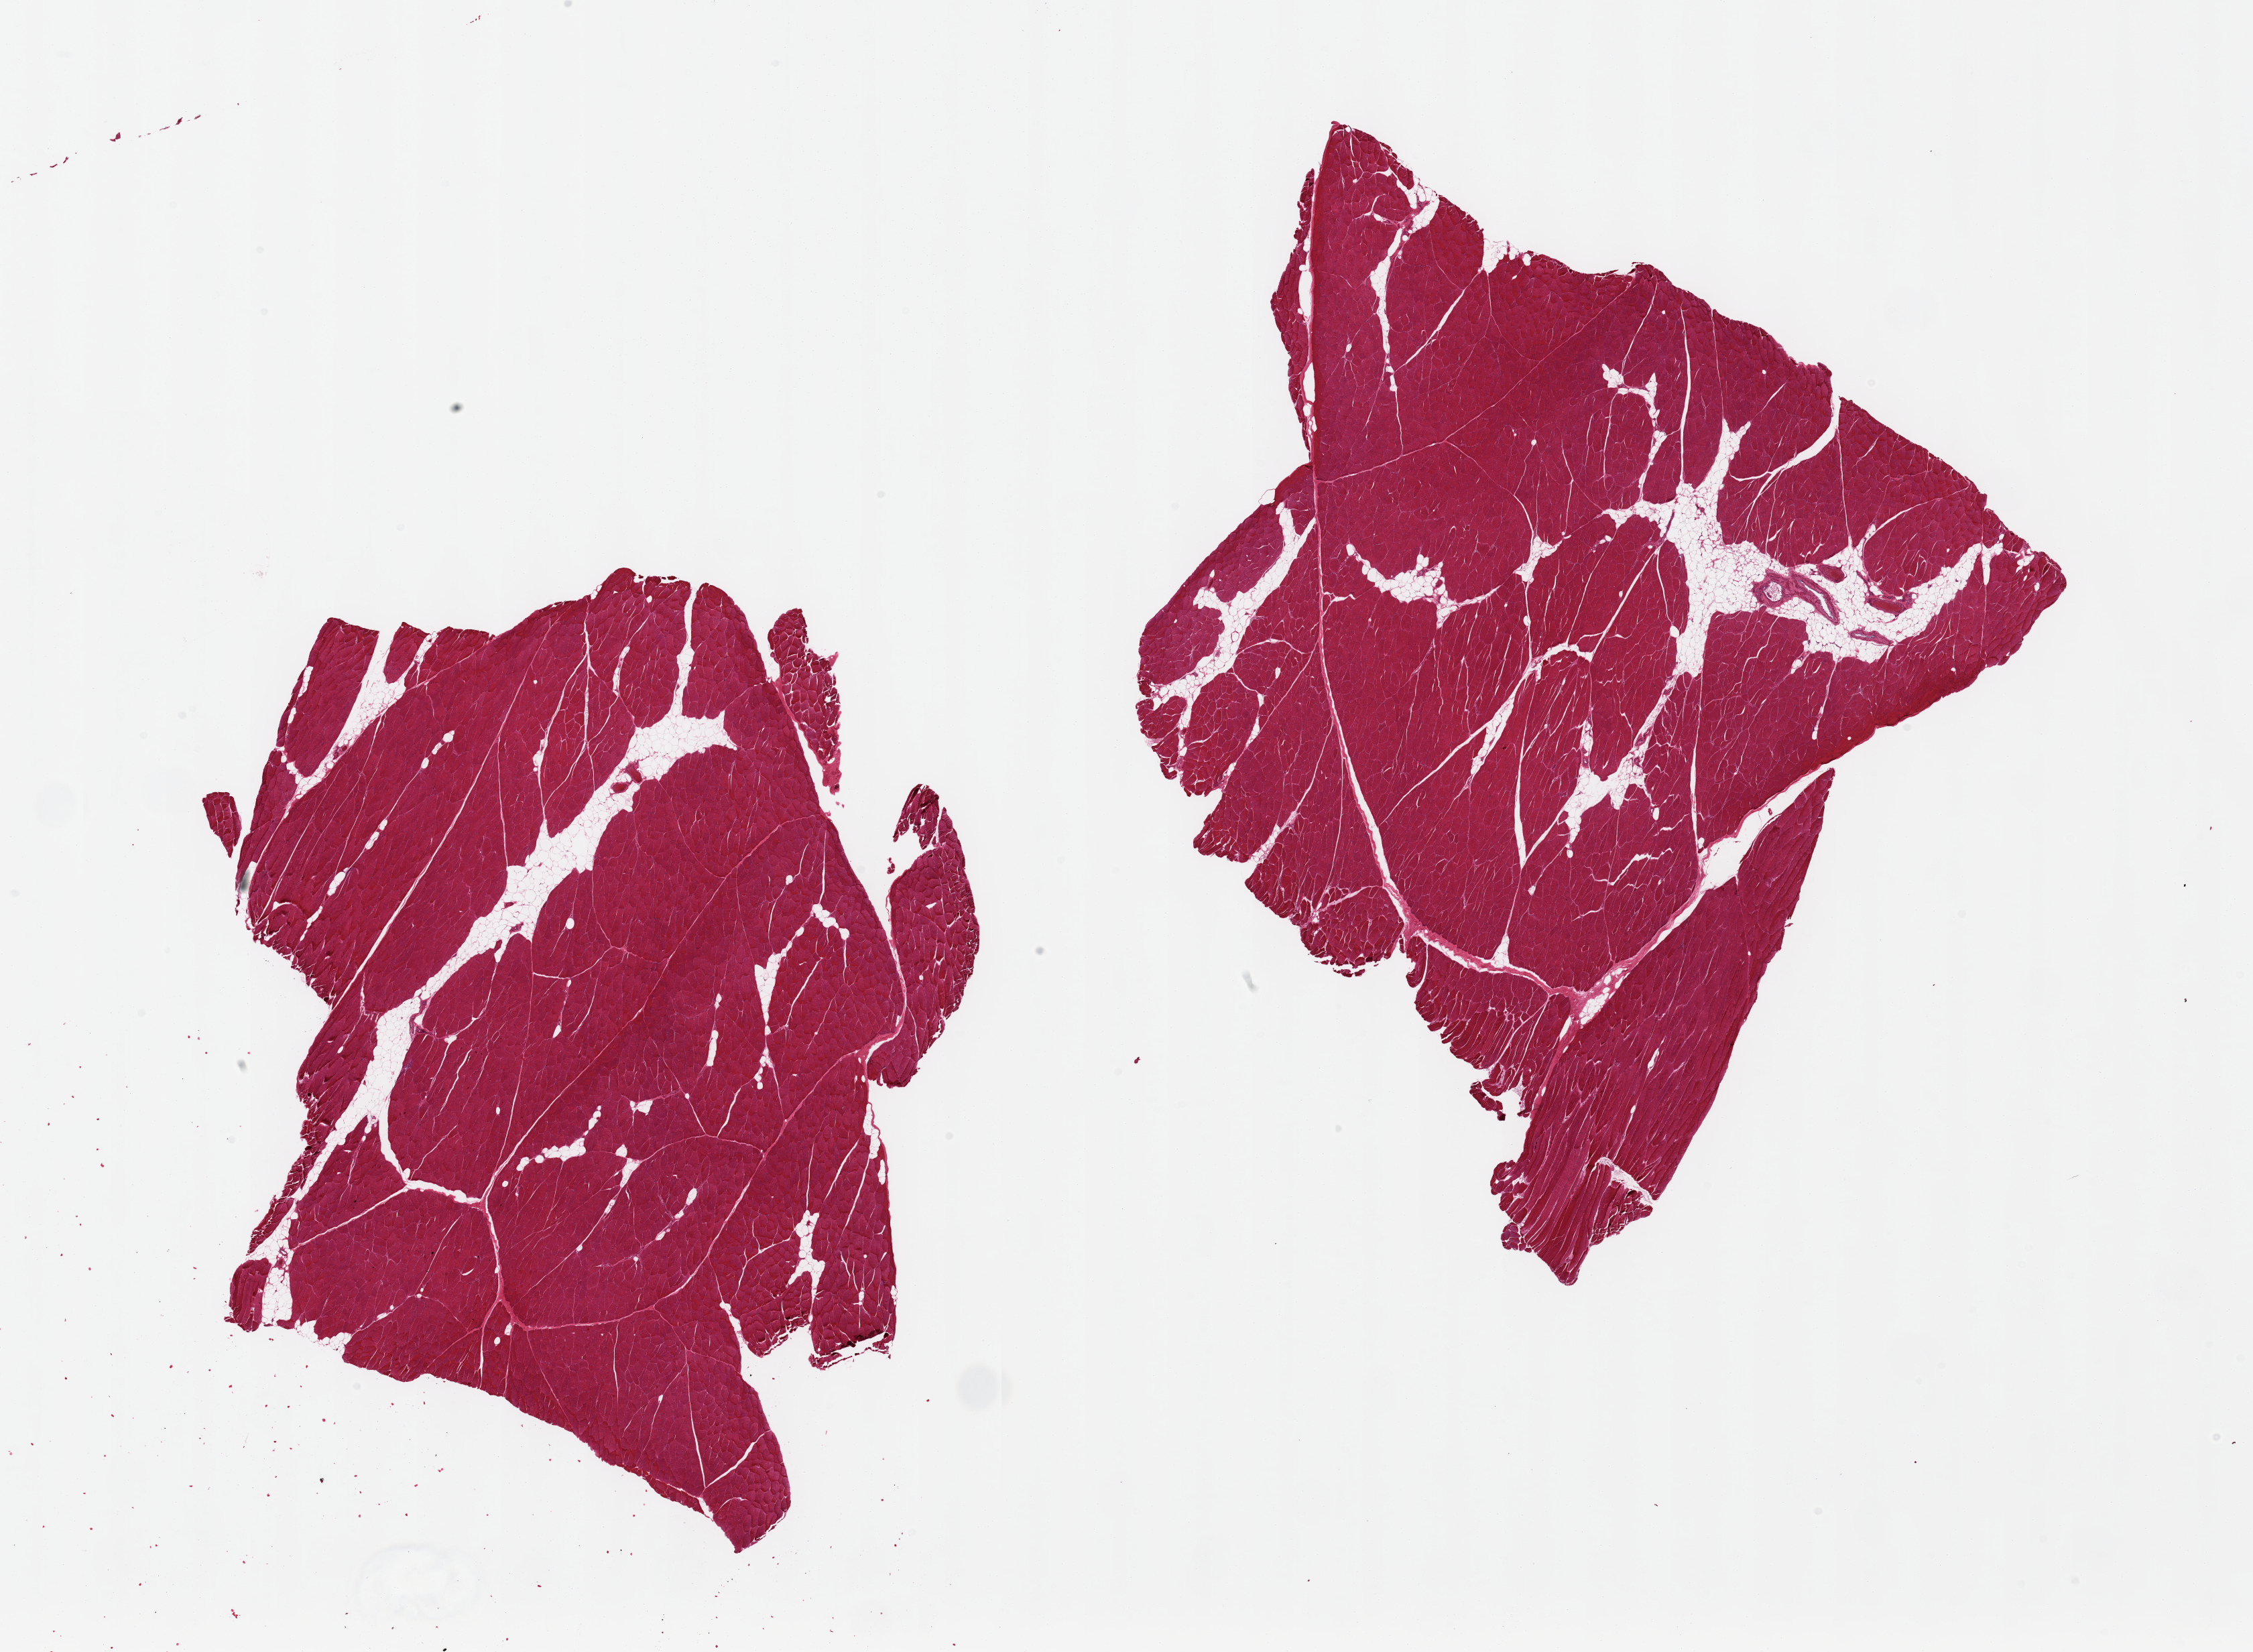
Whole-slide image, haematoxylin and eosin stain, brightfield, shown as a low-resolution overview of the whole scanned area (about 26.6 x 19.5 mm); PAXgene-fixed paraffin-embedded (PFPE) section; sampled site (target tissue): skeletal muscle; donor tissue sample. Donor sex: male.
• reviewer comment on this tissue sample: 2 pieces, ~10-15% interstitial fat